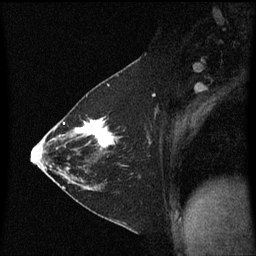
Breast MRI (dynamic contrast-enhanced), one sagittal slice; position 34 of 60 along the scan axis; dynamic contrast-enhanced series, image 2 of 3 at this slice position (ordered by acquisition); 1.5 T; TE 4.2 ms, TR 8.4 ms; 2 mm slice thickness; 256 × 256 image matrix. Female patient, age 36 years. Case-level facts recorded for this patient, not image findings: setting: breast cancer imaged before/during neoadjuvant chemotherapy; receptor status: HR-positive, HER2-negative.
Annotated regions visible in this slice (semi-automatically segmented with operator editing):
- analysis volume of interest (the breast-tissue region the enhancement analysis was run in; not a lesion): box from (x=72, y=116) to (x=117, y=187) px
- tumour enhancement mask (voxels above the 70 % enhancement threshold inside the analysis volume of interest): (x=72, y=118)–(x=117, y=187)